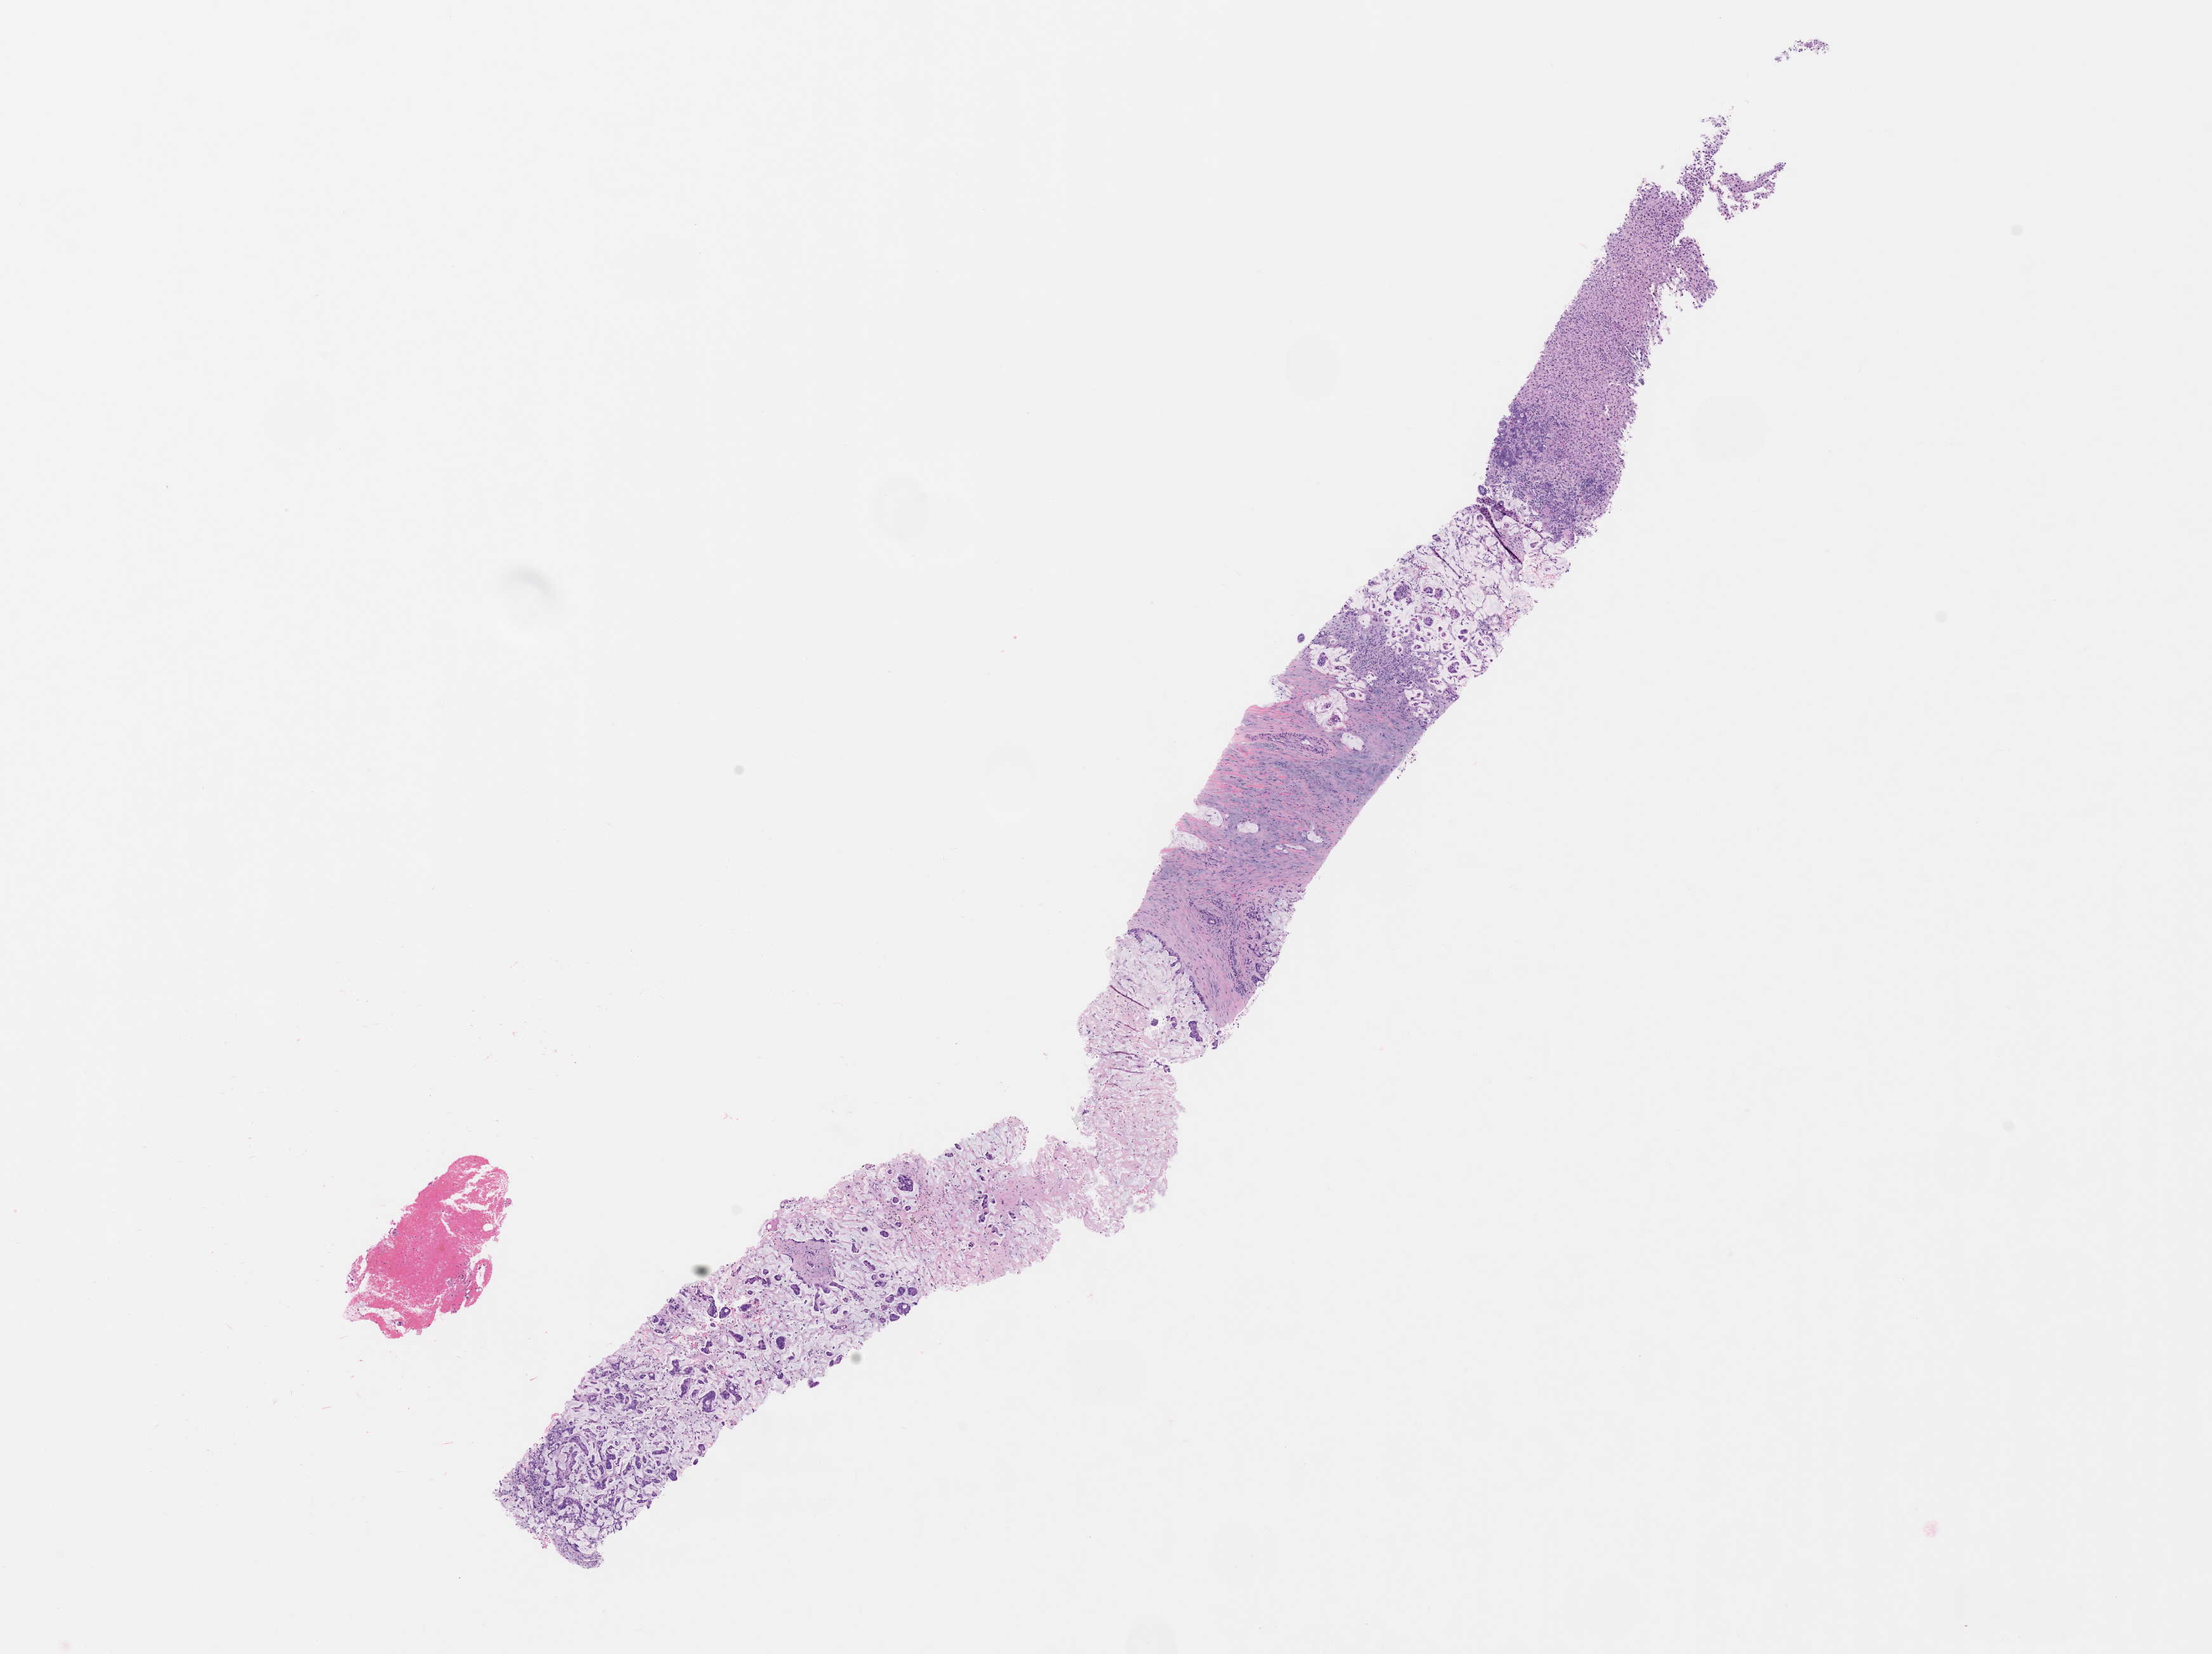
H&E whole-slide image of the patient's (originator) tumor tissue, low-resolution overview of the scanned area, about 14.0 x 10.5 mm. Formalin-fixed, paraffin-embedded (FFPE) tissue. Originating tumor site category: small intestine. Patient male; 49 years old.
Diagnosis: Small Intestinal Adenocarcinoma.